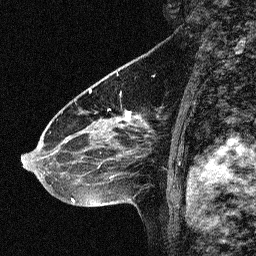
Breast MRI (dynamic contrast-enhanced), one sagittal slice; position 40 of 64 along the scan axis; dynamic contrast-enhanced study with each time point stored as its own series, time point 2 of 3 at this slice position (early post-contrast, ordered by acquisition time); 1.5 T; TE 4.5 ms, TR 11 ms; 256 × 256 image matrix. Patient: female, 46 years. From the clinical record (not read from this slice): setting: breast cancer imaged before/during neoadjuvant chemotherapy; receptor status: HER2-positive.
Outlined on this slice (semi-automatic segmentation, software-assisted and operator-edited):
- analysis volume of interest (the breast-tissue region the enhancement analysis was run in; not a lesion): bounding box [x1, y1, x2, y2] px = [42, 80, 150, 180]
- tumour enhancement mask (voxels above the 90 % enhancement threshold inside the analysis volume of interest): [71, 112, 146, 180]